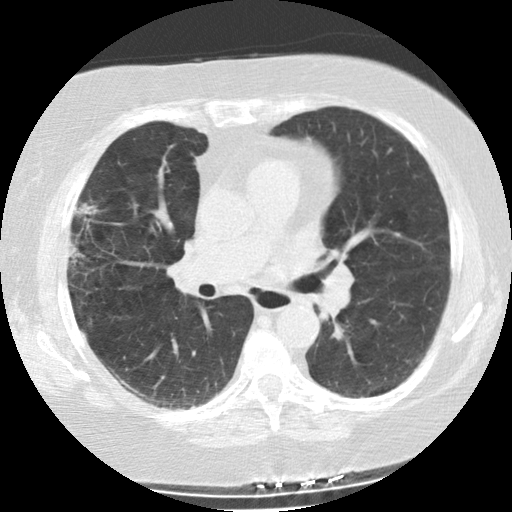
Axial slice from a low-dose chest CT screening exam. Second screening round (one year after baseline). Lung window (W 1500 / L -600 HU). 2.5 mm slice thickness. 120 kVp. Slice 97 of 225 in the series. Female, age 73 years at enrolment.
Expert reader's lesion annotation, box from (x=57, y=195) to (x=104, y=274) px. The screening reader recorded 2 non-calcified nodules or masses ≥4 mm on this exam (right upper lobe, left upper lobe); which of them this box marks is not recorded. Later outcome: lung cancer diagnosed 47 days after this screen — bronchiolo-alveolar adenocarcinoma, NOS, right upper lobe, moderately differentiated (G2), stage IIIB (AJCC 6th edition), 21 mm at pathology.